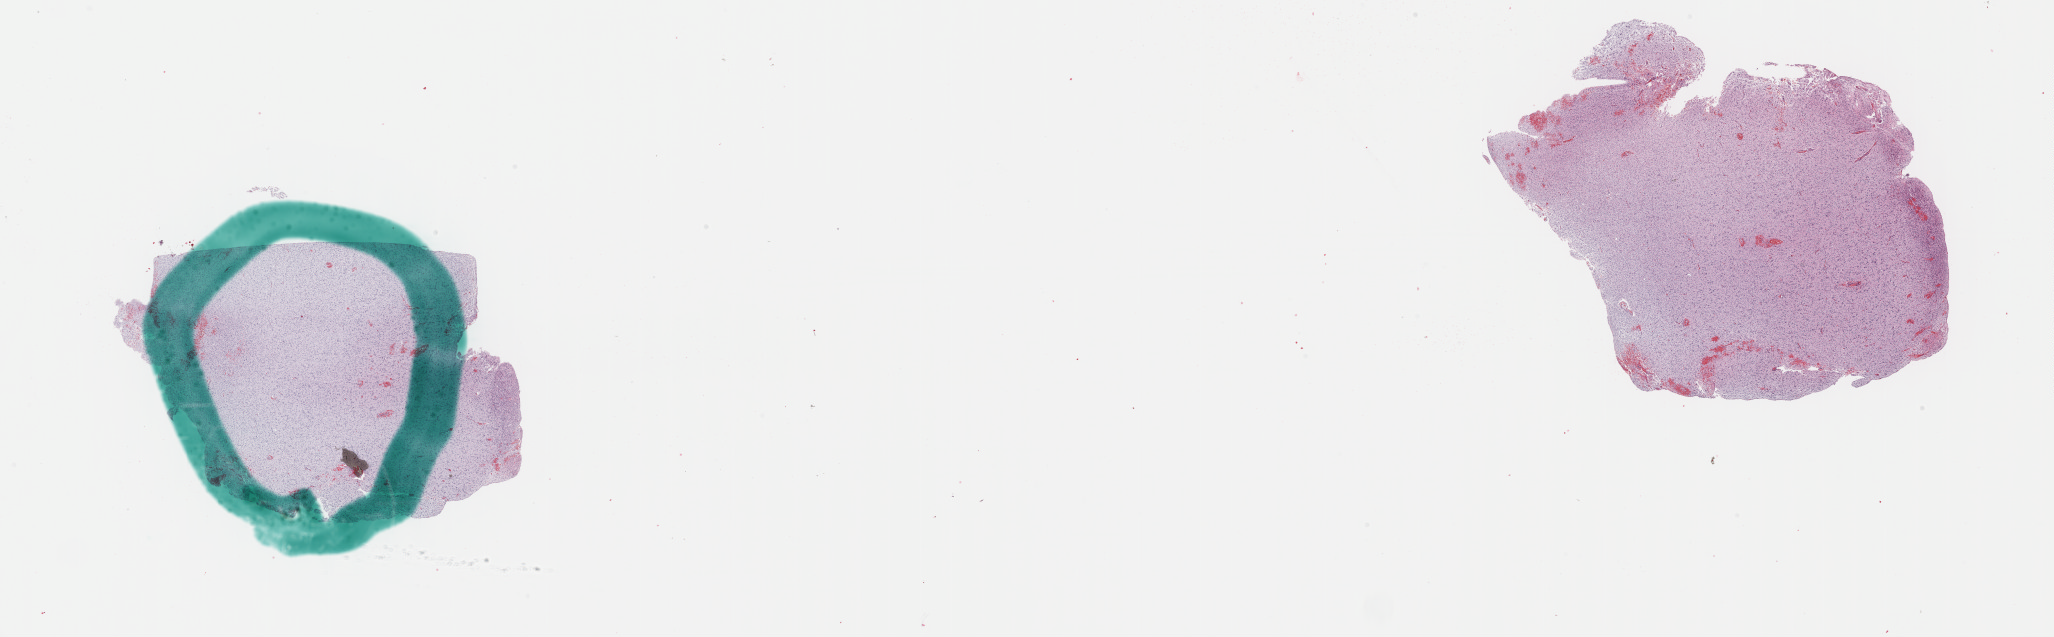
Whole-slide histology image, H&E-stained — shown as a low-resolution overview of the whole scanned area (about 33.2 x 10.3 mm, slide scanned at 40x), formalin-fixed paraffin-embedded (FFPE) diagnostic section, primary tumour sample from the brain. Female, age 50 years at initial diagnosis.
Pathologic diagnosis: Oligodendroglioma, NOS (cerebrum).